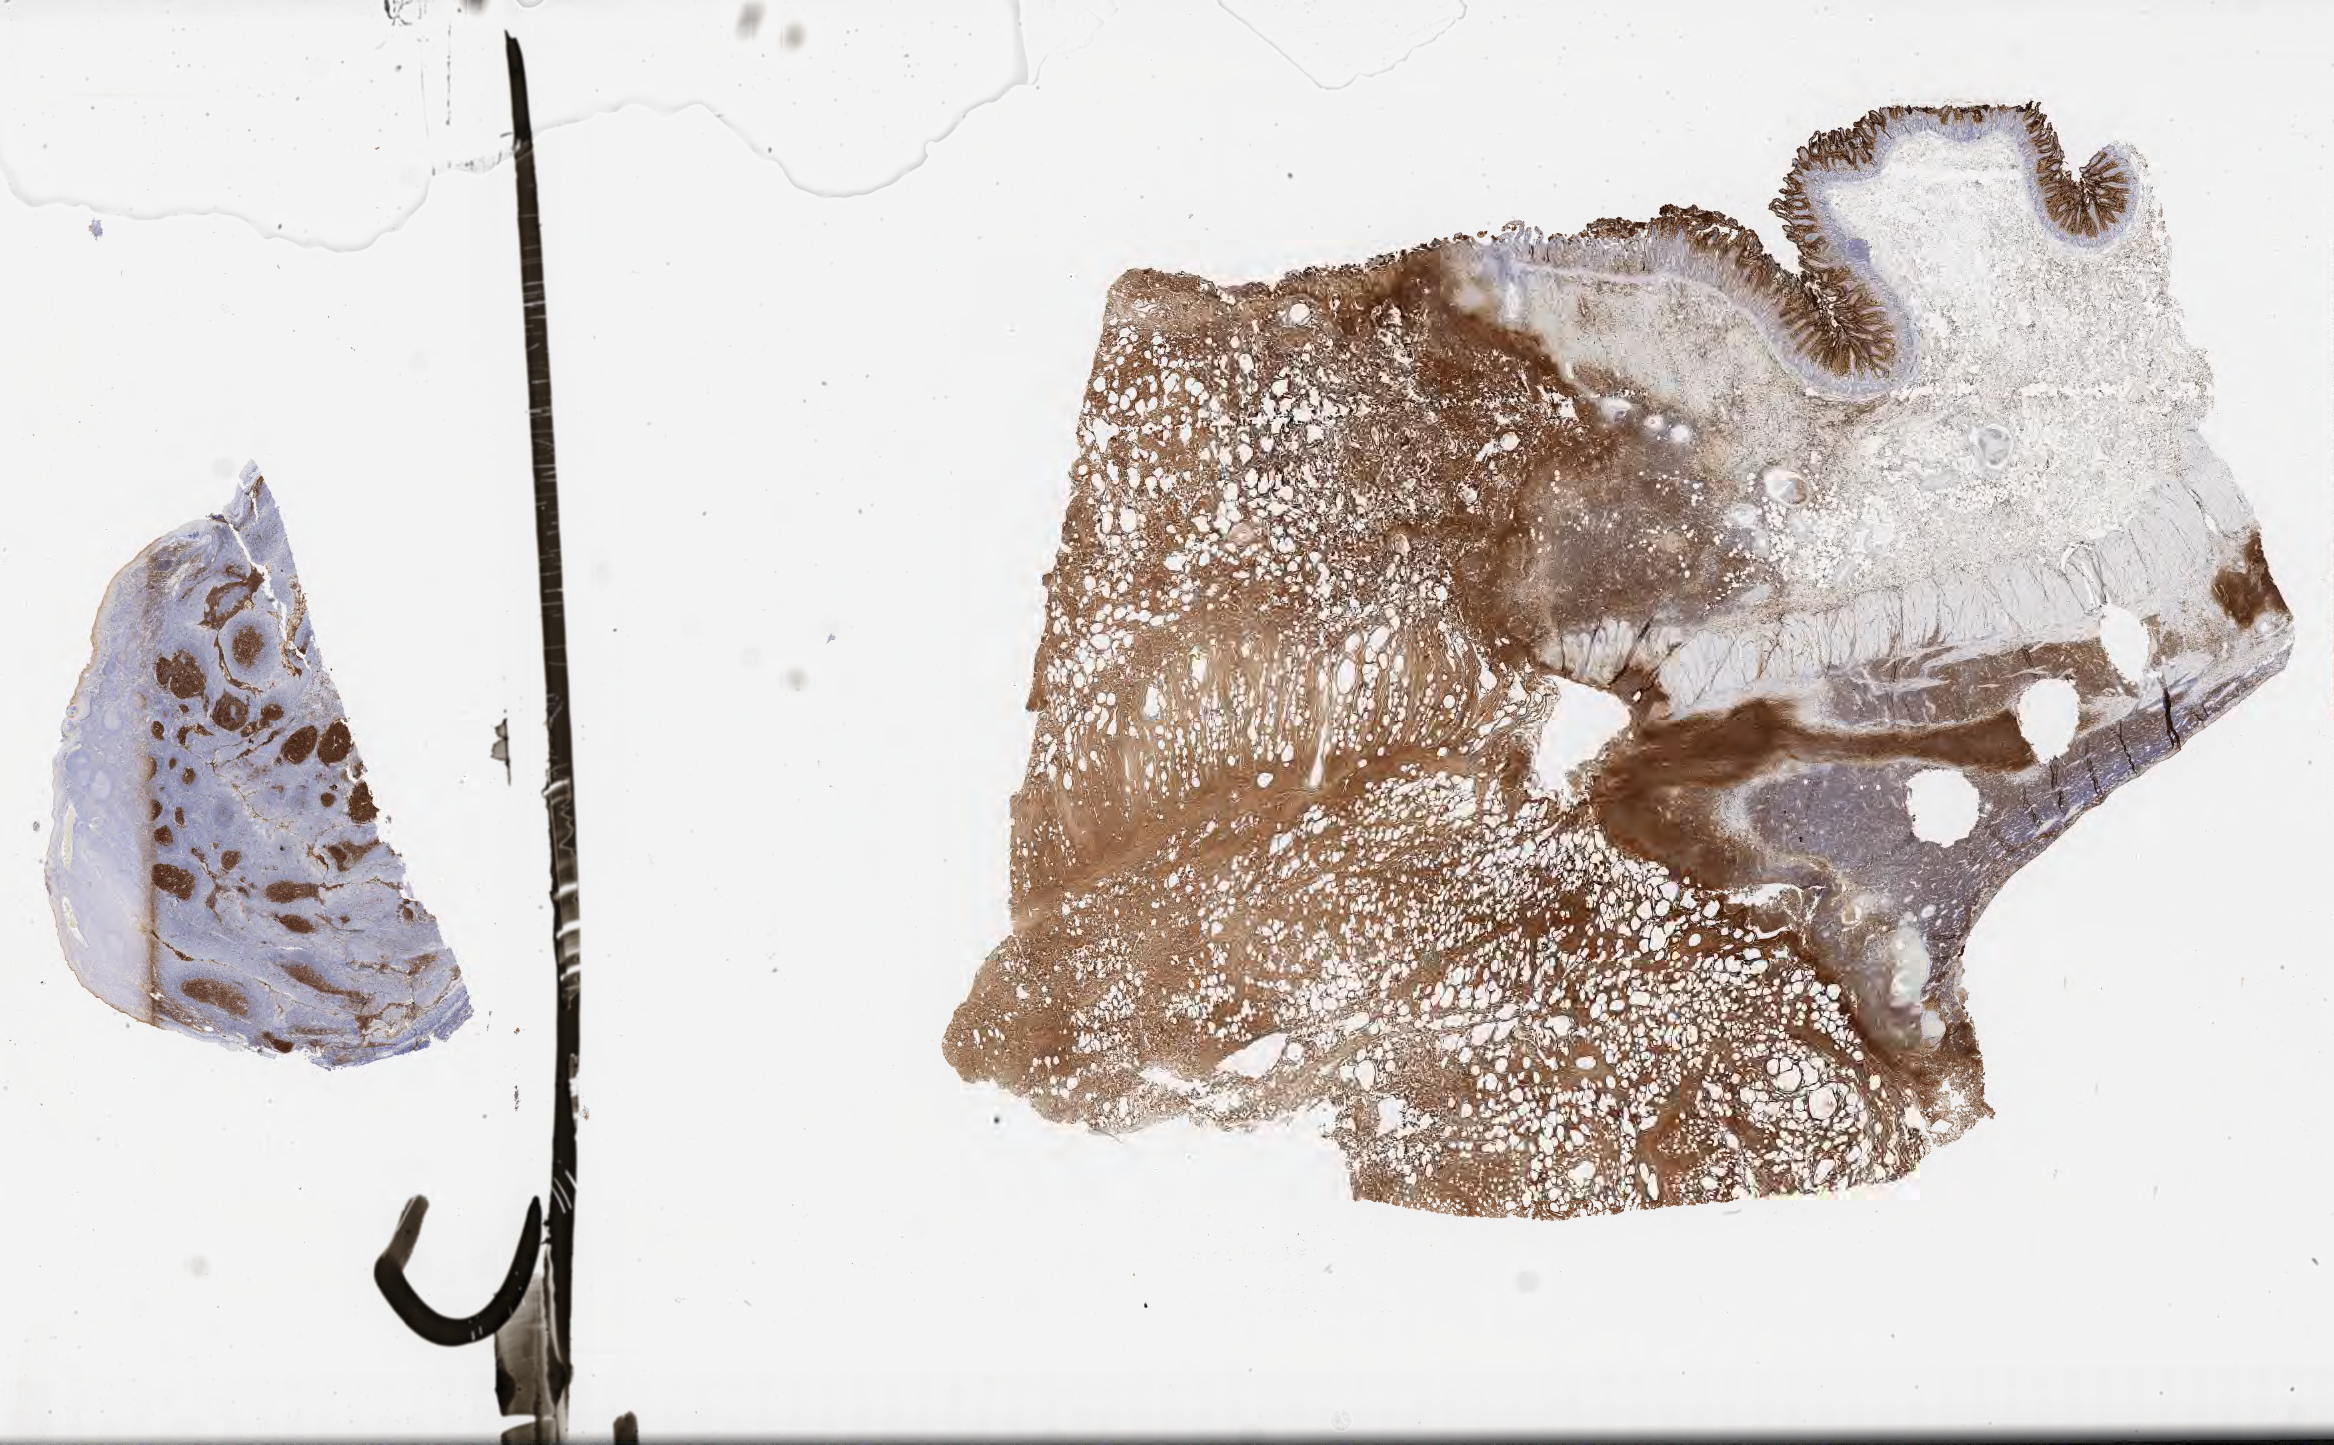
Immunohistochemistry (IHC) whole-slide image stained for CD10, a low-resolution overview of the entire scanned area, about 37.7 x 23.4 mm, tumor tissue, site: colon. Male patient, age 62 years.
Histologic diagnosis: Burkitt lymphoma, NOS.